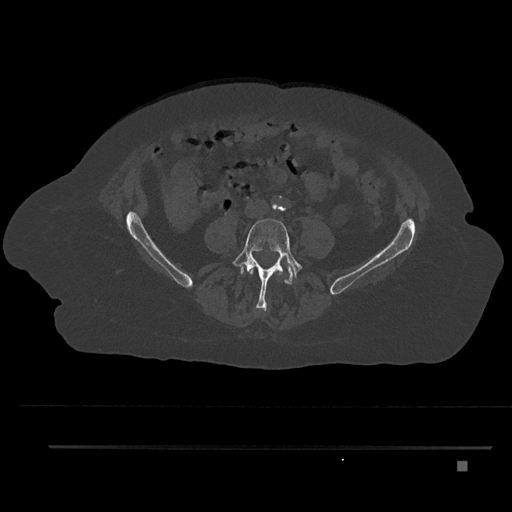
CT including the spine, one axial slice; slice 80 of 797 in the series (ordered by position); reconstruction kernel Br40s/3; bone window (W 1800 / L 400 HU); 512 × 512 image matrix. Patient: female, 76 years. Case-level facts recorded for this patient, not image findings: primary cancer: lung.
Outlined on this slice (semi-automatic segmentation, software-assisted and operator-edited):
- L3 vertebra: box from (x=249, y=268) to (x=282, y=278) px
- L4 vertebra: (x=232, y=218)–(x=304, y=311)
- L5 vertebra: (x=241, y=263)–(x=296, y=284)